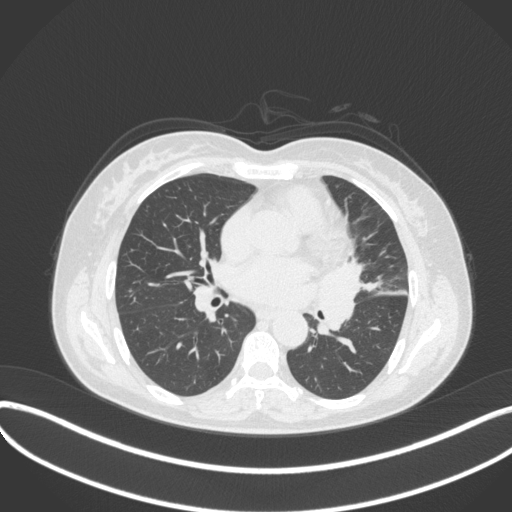
Chest CT, one axial slice; position 177 of 373 along the scan axis; reconstruction kernel B31f; lung window (W 1500 / L -600 HU); 512 × 512 image matrix, field of view 400 × 400 mm. Patient: female, 54 years. Case-level facts recorded for this patient, not image findings: clinical TNM (as recorded): T2a N1 M0; histopathological grade: G3.
Annotated regions visible in this slice (rectangle marked by the reading radiologist):
- lung tumour (recorded histology: small cell carcinoma): bounding box <318,255,376,342> (left, top, right, bottom; pixels)